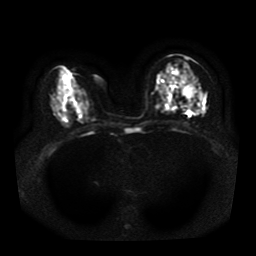
Breast MRI, one axial slice. Slice 17 of 41 in the series (ordered by position). Diffusion-weighted series; image 2 of 4 stored at this slice position (different b-values; order by instance number). 1.5 T. 5 mm slice thickness. 256 × 256 image matrix, field of view 330 × 330 mm. Female patient.
Outlined on this slice (expert manual segmentation):
- tumour on diffusion-weighted imaging: bounding box <172,70,204,113> (left, top, right, bottom; pixels)